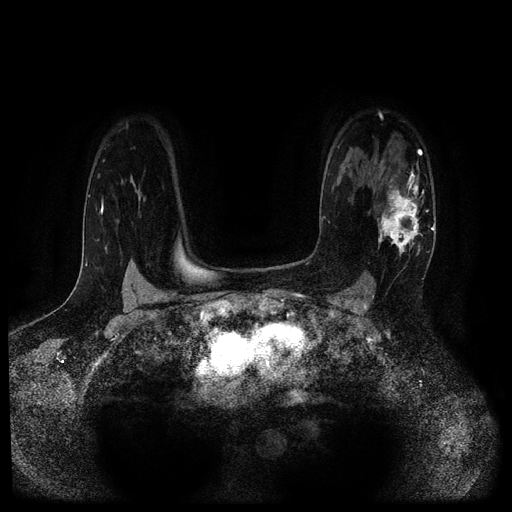
Breast MRI (dynamic contrast-enhanced, multi-phase), one axial slice; position 76 of 116 along the scan axis; dynamic contrast-enhanced series, time point 2 of 5 at this slice position (early post-contrast); 1.5 T; TE 2.7 ms, TR 5.4 ms; 512 × 512 image matrix, field of view 330 × 330 mm. Patient: female, 43 years.
Annotated regions visible in this slice (semi-automatically segmented with operator editing):
- breast lesion (labelled 'tumour' in the annotation; benign lesions carry a separate 'benign' label): bounding box [x1, y1, x2, y2] px = [375, 164, 429, 268]